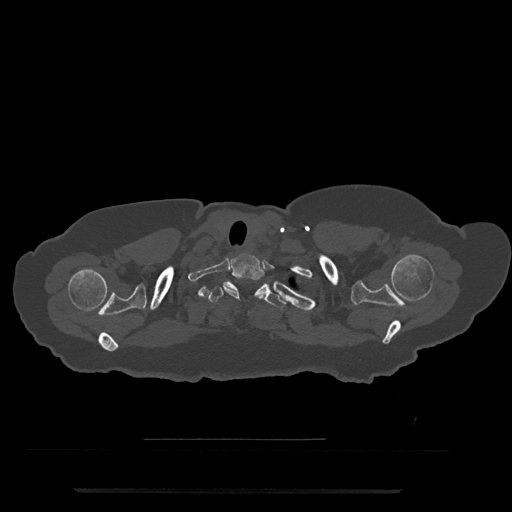
CT including the spine, one axial slice; slice 694 of 797 in the series (ordered by position); 120 kVp; bone window (W 1800 / L 400 HU); 512 × 512 image matrix. Patient: female, 51 years. Case-level facts recorded for this patient, not image findings: primary cancer: neuro.
Structures marked on this image (semi-automatically segmented with operator editing):
- T1 vertebra: bounding box (x1, y1, x2, y2) in pixels: (223, 254, 265, 299)
- T2 vertebra: (207, 281, 286, 309)